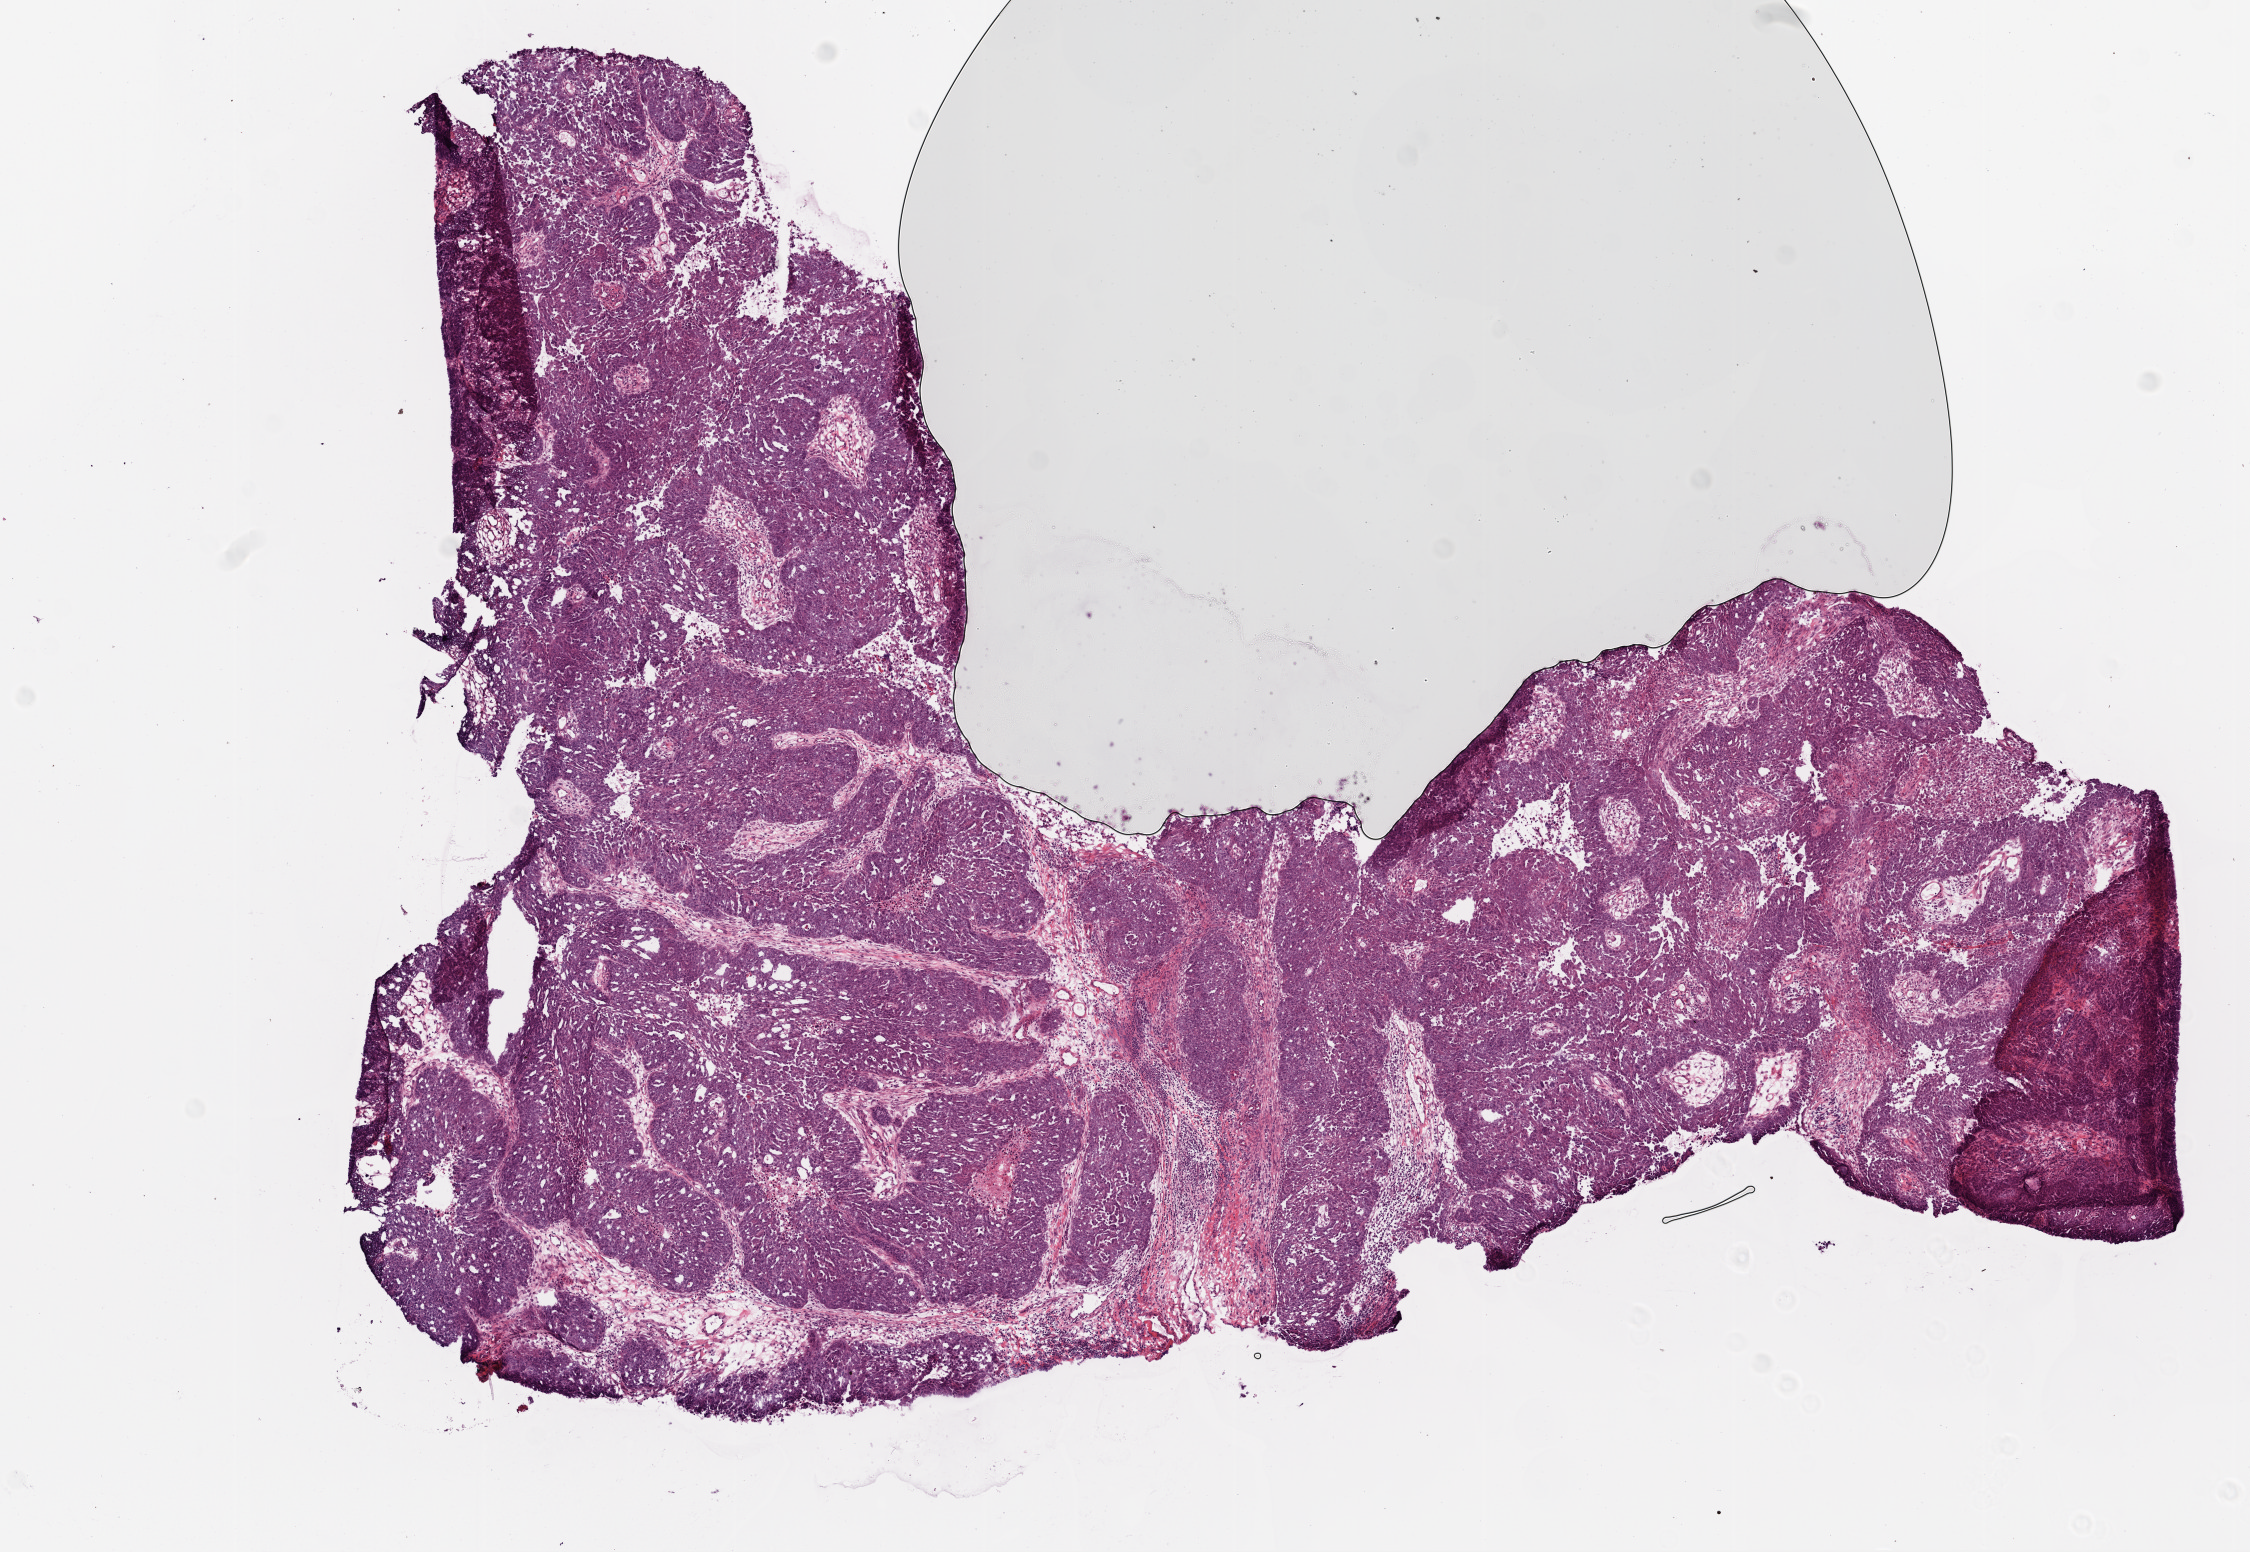
Whole-slide histology image, H&E, a low-resolution overview of the entire scanned area, about 9.0 x 6.2 mm (slide scanned at 20x); frozen section from the top of the tissue portion; ovary, primary tumour sample. Female, age 61 years at initial diagnosis. Histologic grade: G2 (moderately differentiated). Composition of this section per pathologist review: tumour cells 83%, tumour nuclei 90%, normal cells 5%, stromal cells 7%, necrosis 5%.
FIGO stage: IIC. Laterality: bilateral. Pathologic diagnosis: Serous cystadenocarcinoma, NOS.